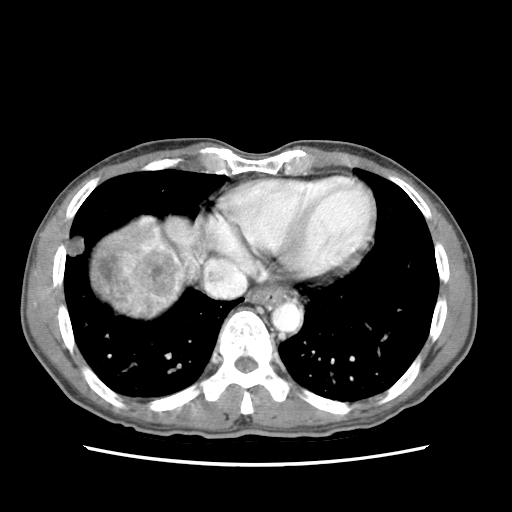
Contrast-enhanced abdominal CT (liver protocol), one axial slice. Position 70 of 79 along the scan axis. Reconstruction kernel STANDARD. 120 kVp. Soft-tissue window (W 400 / L 40 HU). 512 × 512 image matrix. From the clinical record (not read from this slice): diagnosis: hepatocellular carcinoma (patient treated with transarterial chemoembolisation; whether this scan precedes or follows treatment is not stated here); TNM stage (as recorded): Stage-IIIB.
Annotated regions visible in this slice (semi-automatically segmented with operator editing):
- liver parenchyma outside the tumour (the mass and vessels are separate outlines, so this box may not span the whole liver): bounding box [x1, y1, x2, y2] px = [88, 214, 208, 316]
- mass: [91, 218, 183, 316]
- liver vessels: [141, 217, 199, 305]